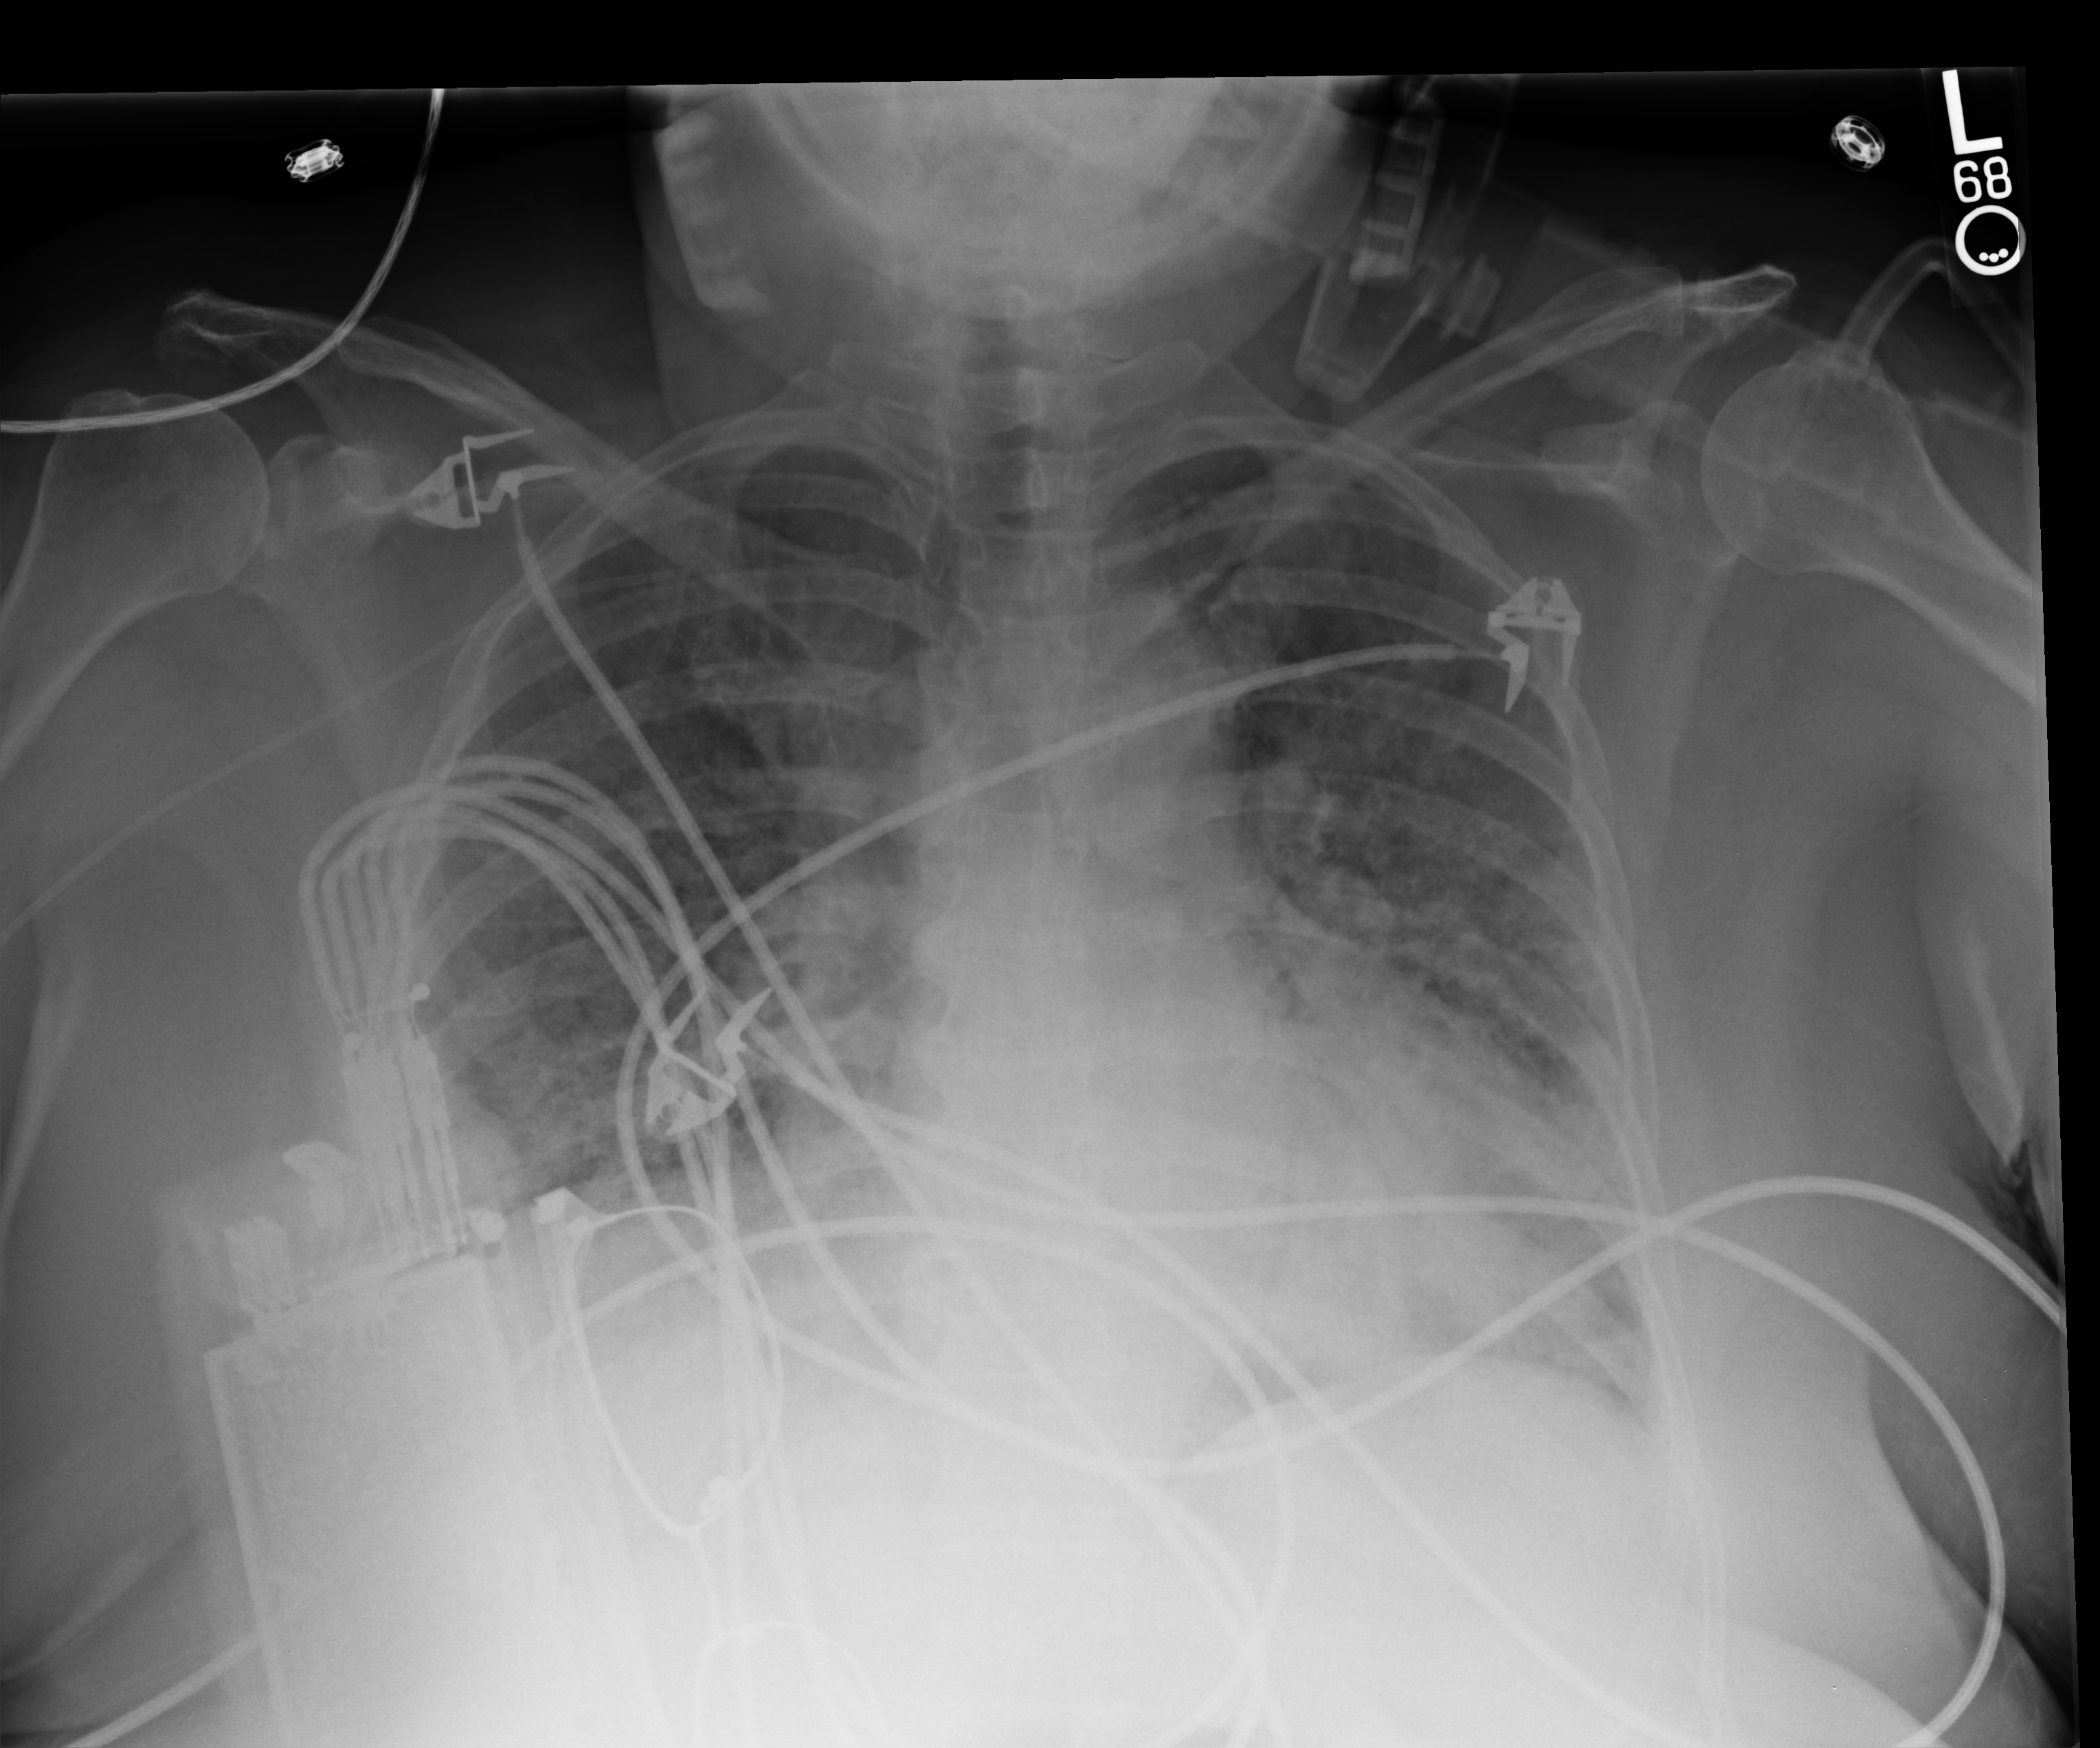
Chest X-ray (portable), anteroposterior (AP) projection. Female patient hospitalised with COVID-19, age 60–74 years.
Admission-level facts for this patient (not findings on this image; timing relative to this image not recorded): hypertension (admission record): no.